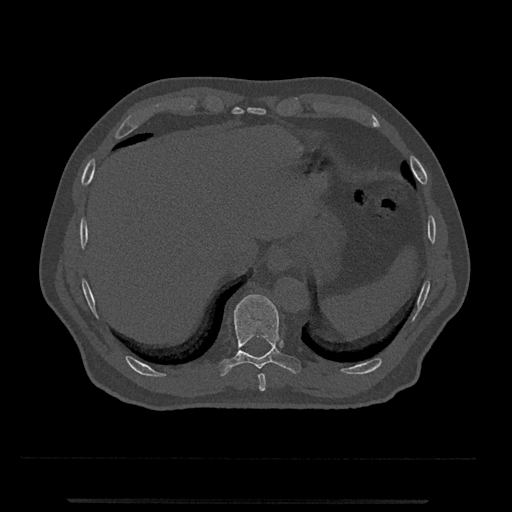
CT including the spine, one axial slice; position 523 of 797 along the scan axis; reconstruction kernel Br40s/3; 120 kVp; bone window (W 1800 / L 400 HU); 0.5 mm slice thickness; 512 × 512 image matrix, field of view 419 × 419 mm. Patient: male, 63 years. From the clinical record (not read from this slice): primary cancer: prostate.
Annotated regions visible in this slice (semi-automatically segmented with operator editing):
- T10 vertebra: bounding box (x1, y1, x2, y2) in pixels: (218, 294, 301, 376)
- T9 vertebra: (258, 374, 266, 392)